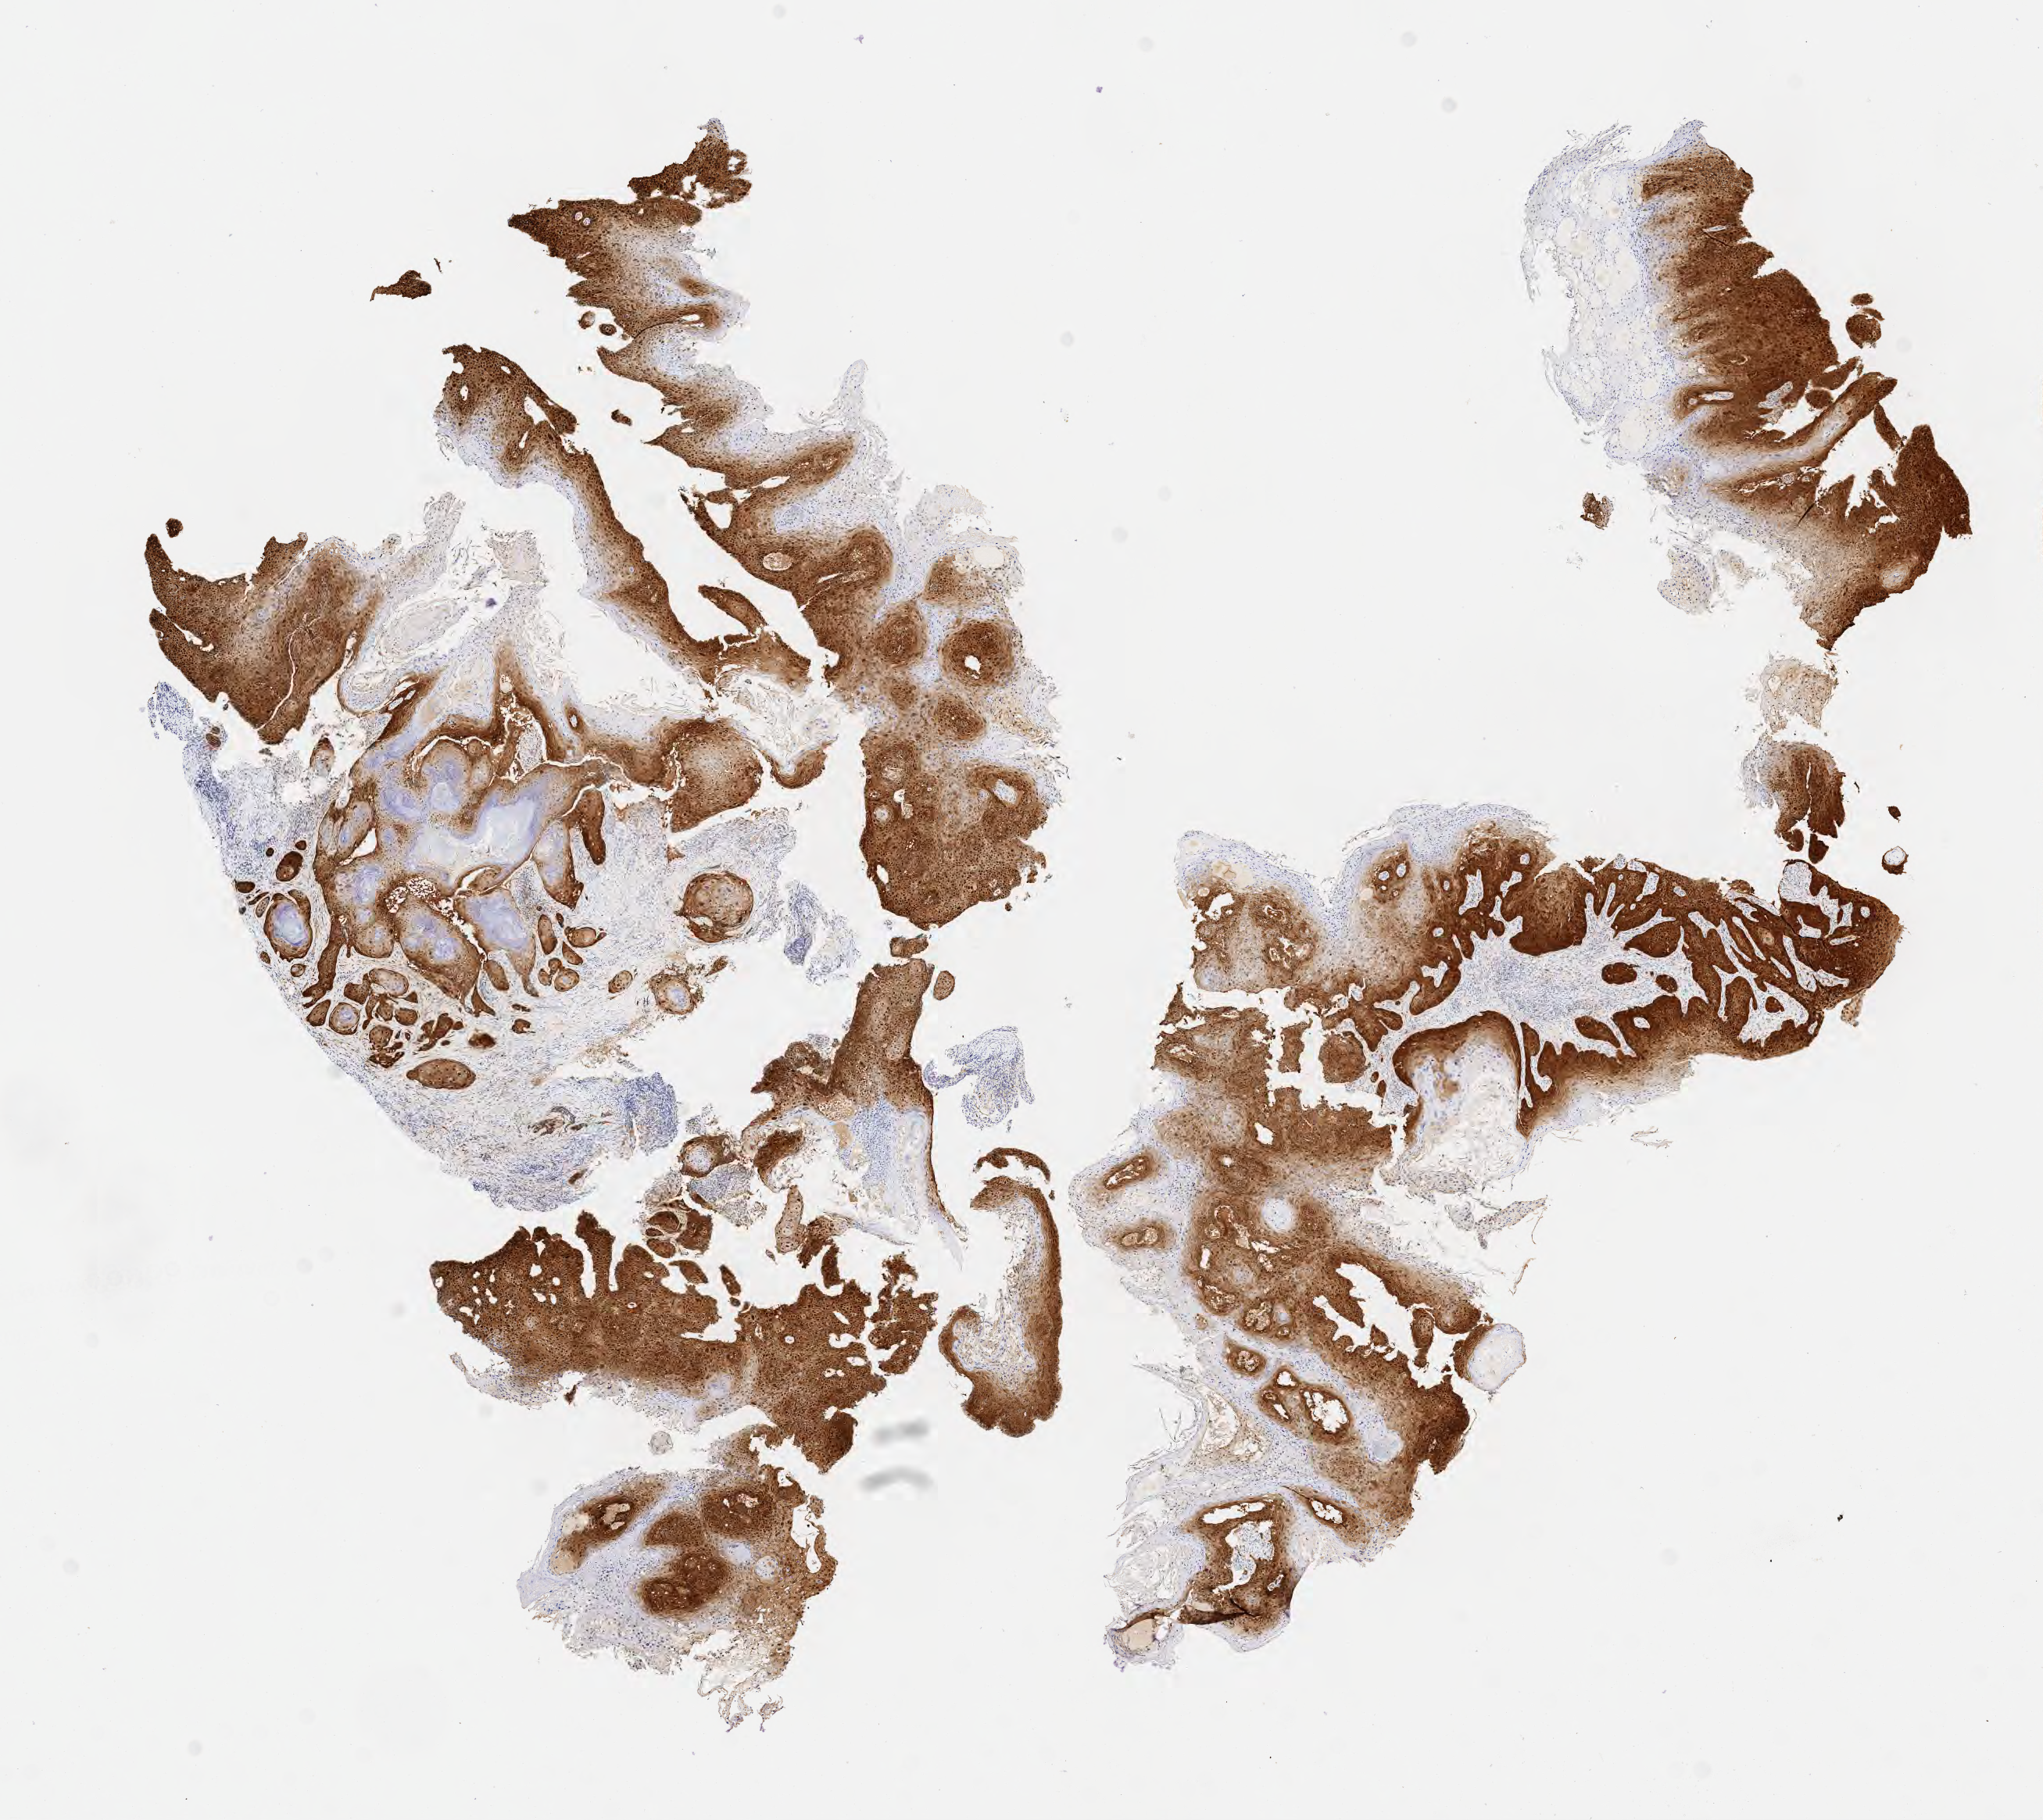
Immunohistochemistry (IHC) whole-slide image stained for p16 (p16INK4a) — shown as a low-resolution overview of the whole scanned area (about 10.6 x 9.4 mm). Specimen: tumor tissue. Site: cervix. Female patient, age 41 years.
Diagnosis: Warty carcinoma.